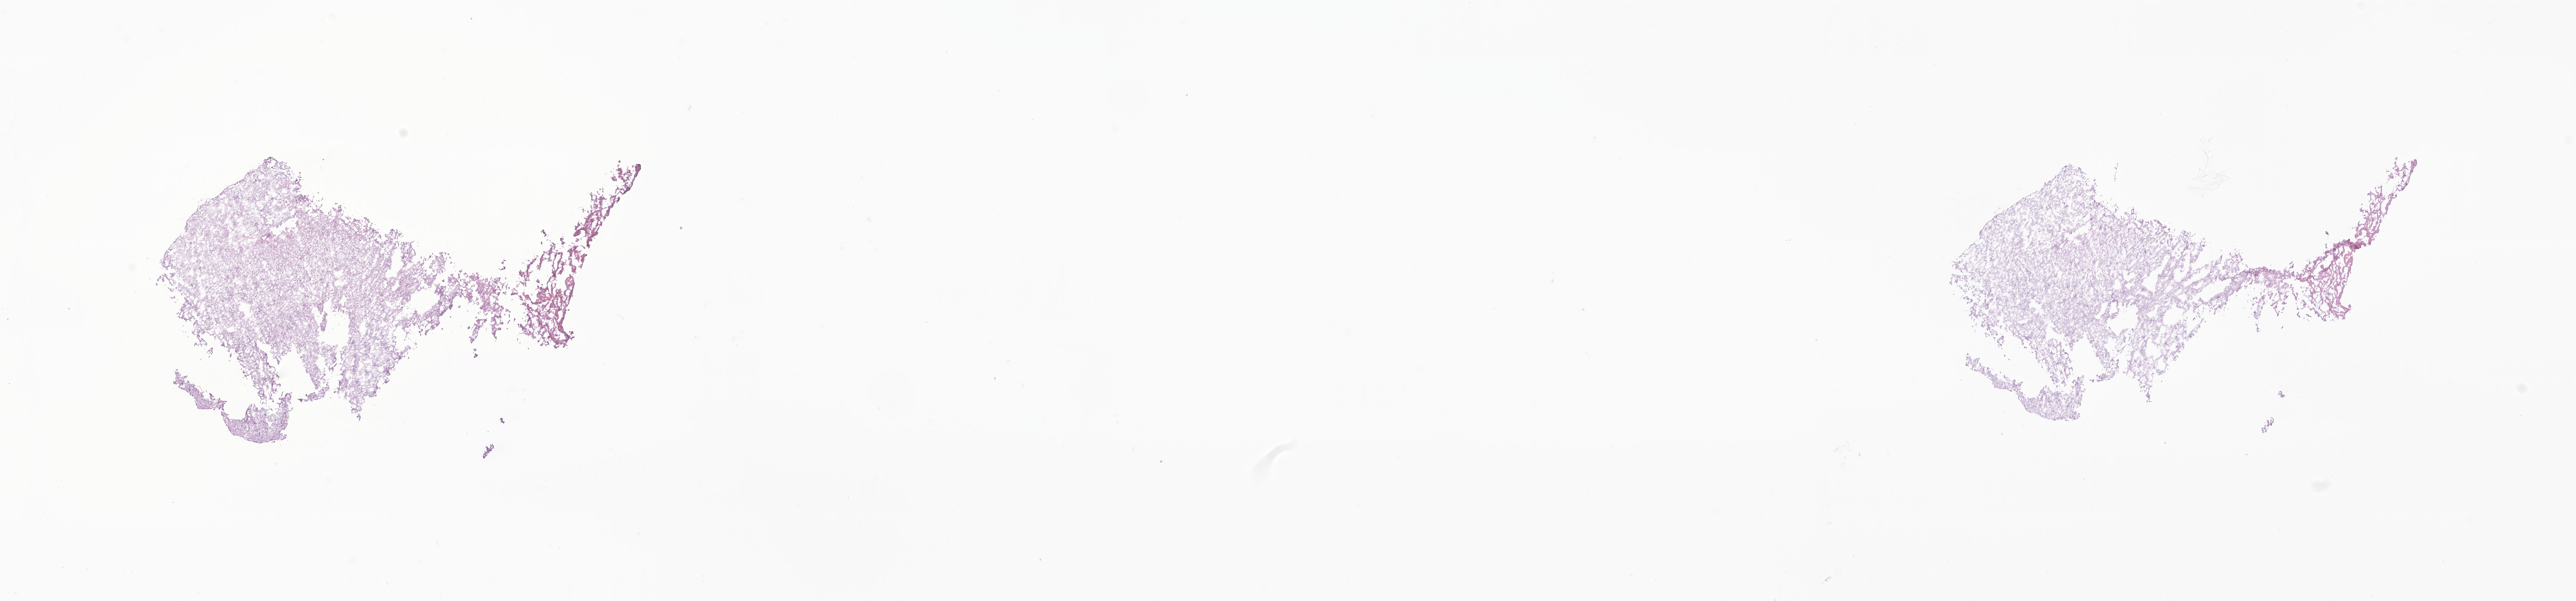
Digitized H&E-stained section of tumor tissue from the brain — whole scanned area (about 30.3 x 7.1 mm) shown as a low-resolution overview. Cryosection (OCT / tissue freezing medium). Patient male; age 78 months (6 years 6 months).
Diagnosis: Pilocytic astrocytoma.